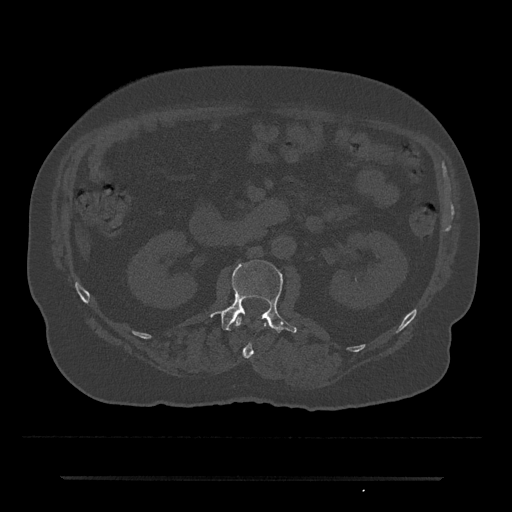
CT including the spine, one axial slice; slice 25 of 797 in the series (ordered by position); reconstruction kernel Br40s/3; 120 kVp; bone window (W 1800 / L 400 HU); 512 × 512 image matrix, field of view 437 × 437 mm. Male patient, age 69 years. From the clinical record (not read from this slice): primary cancer: prostate.
Annotated regions visible in this slice (semi-automatic segmentation, software-assisted and operator-edited):
- L1 vertebra: bounding box [x1, y1, x2, y2] px = [235, 316, 266, 359]
- L2 vertebra: [211, 260, 297, 333]